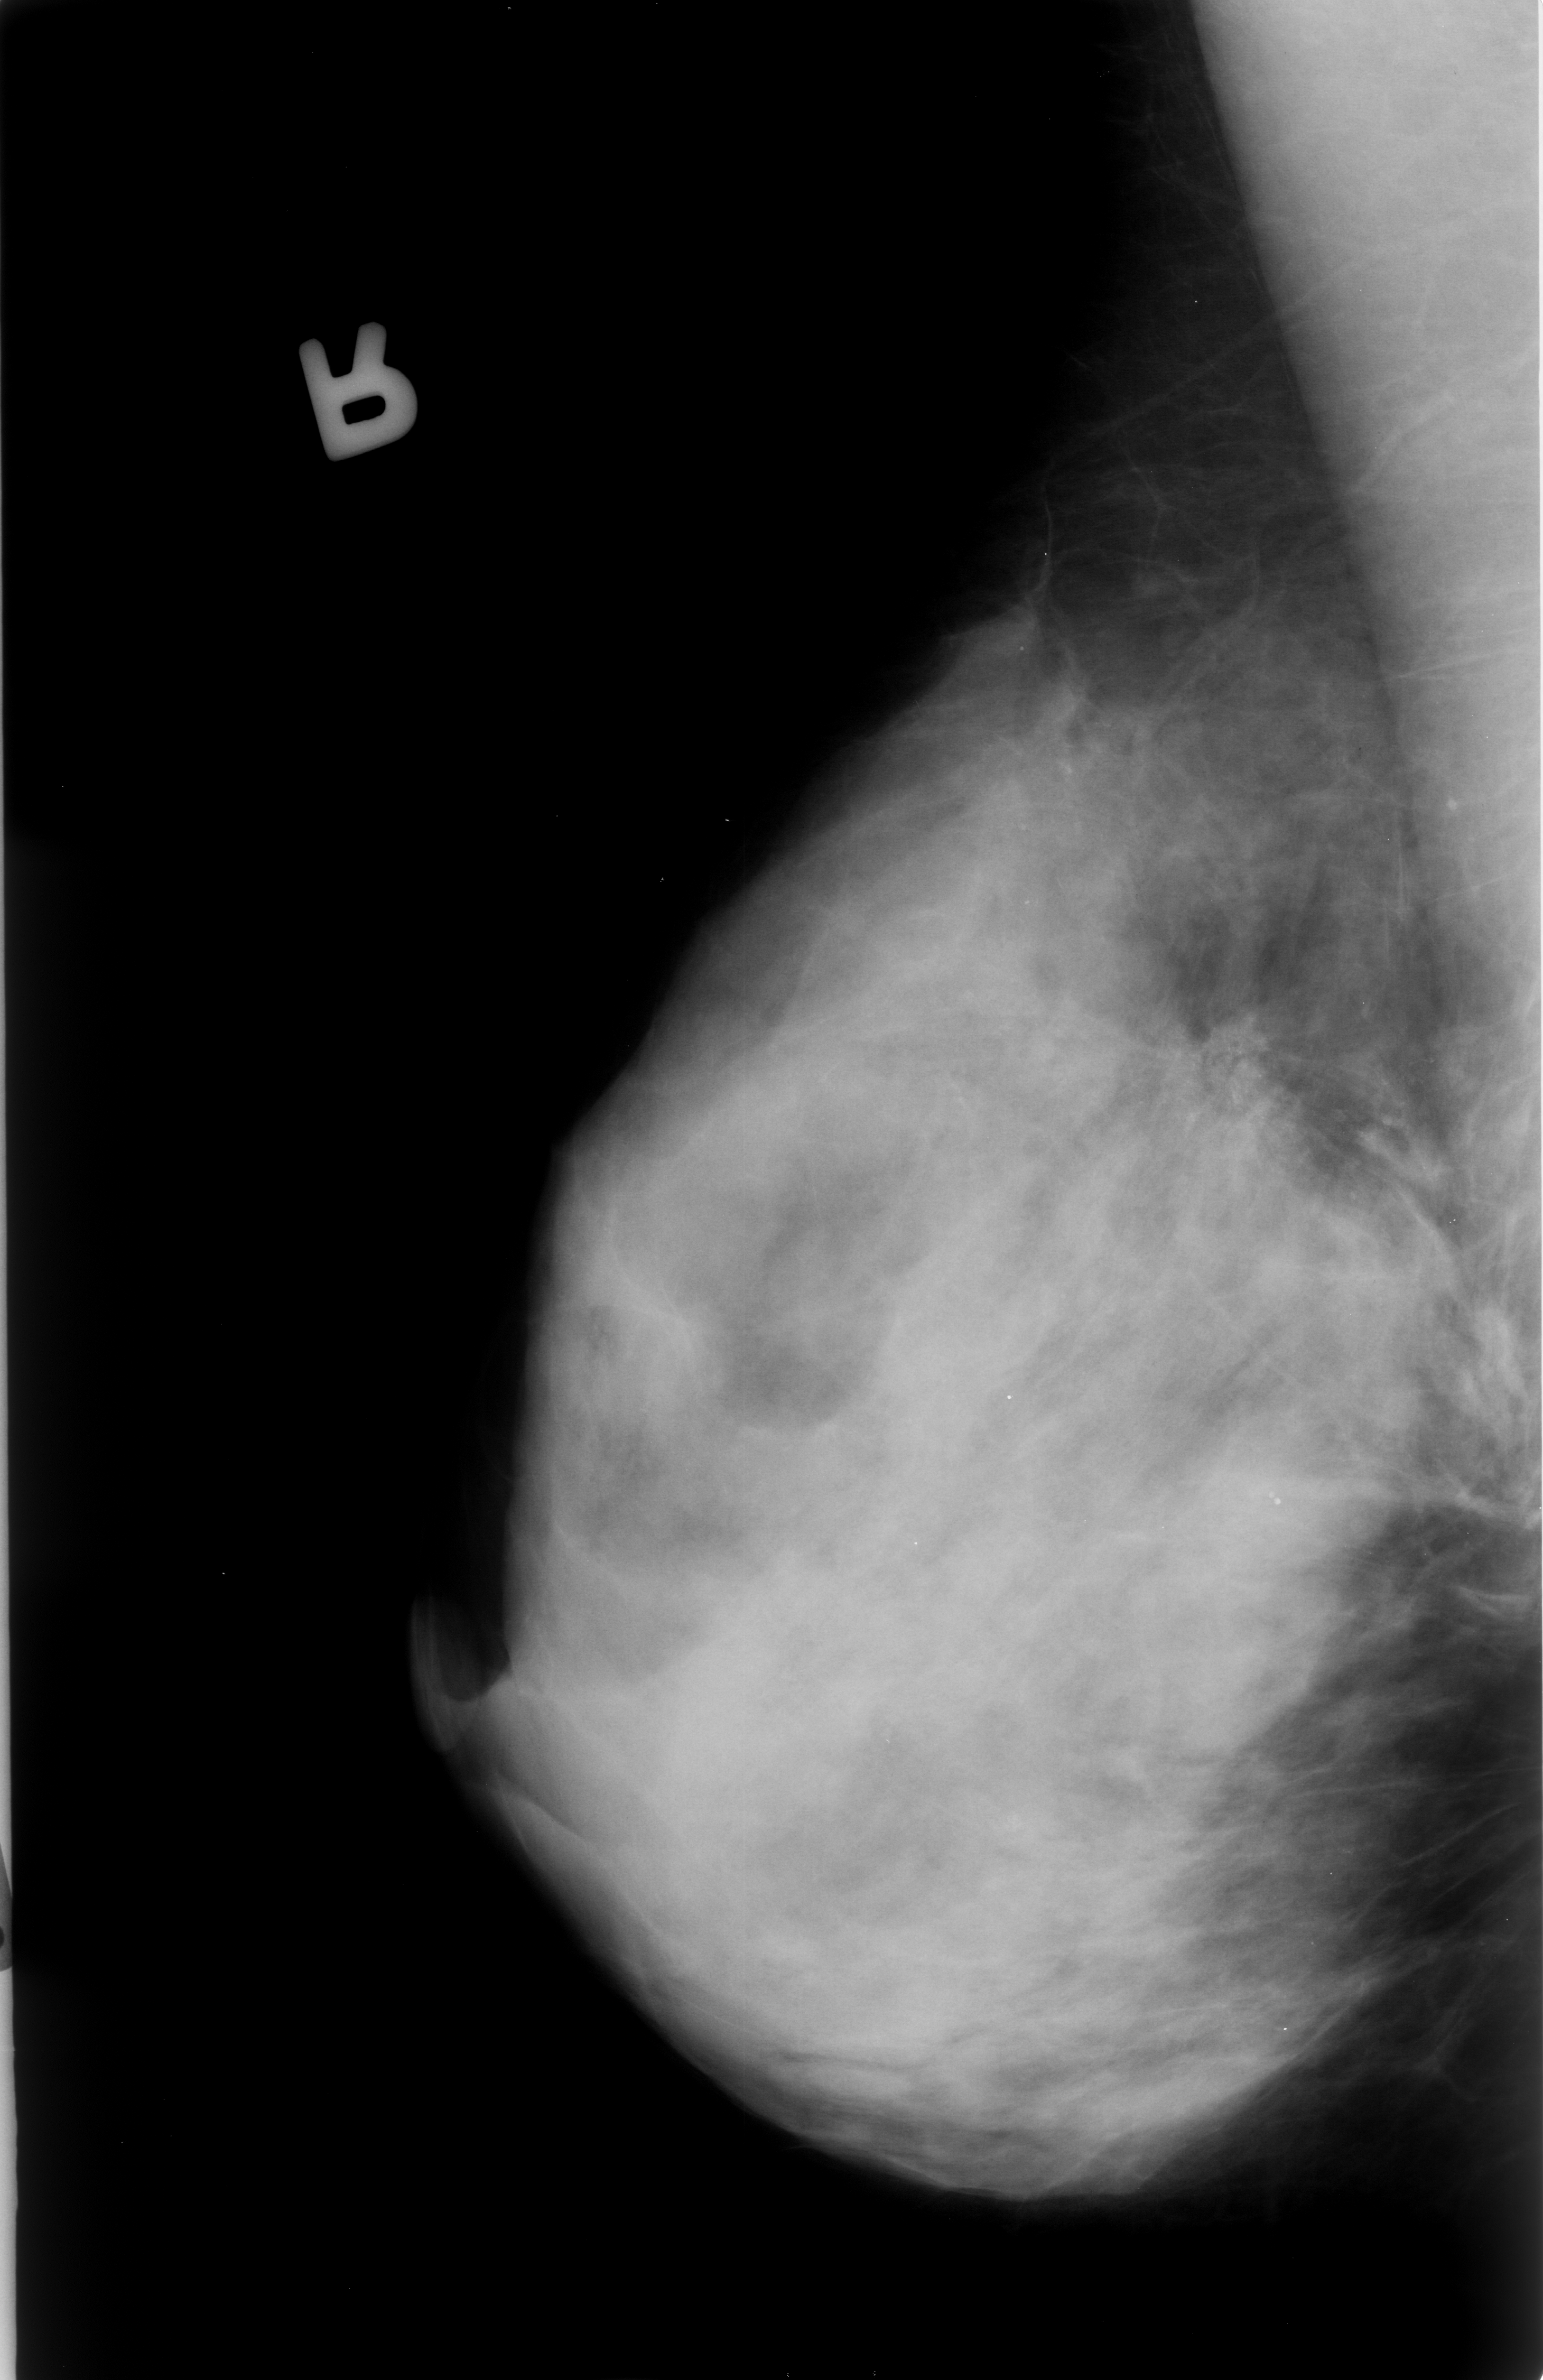
Mammogram (digitized film), right breast, mediolateral oblique (MLO) view, BI-RADS breast density category 4 (scale 1–4).
Marked findings (only marked abnormalities are described; nothing is implied about the rest of the image): calcifications, morphology punctate / pleomorphic, distribution clustered; BI-RADS assessment category 4; pathology result (as recorded, not read from the image): malignant.